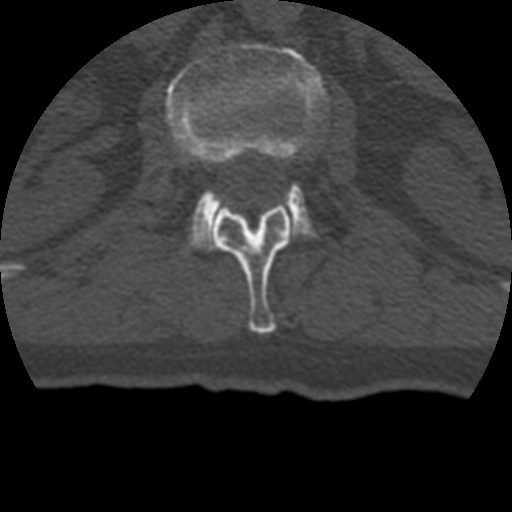
CT including the spine, one axial slice. Slice 133 of 399 in the series (ordered by position). Reconstruction kernel STANDARD. 120 kVp. Bone window (W 1800 / L 400 HU). 1.25 mm slice thickness. 512 × 512 image matrix, field of view 160 × 160 mm. Patient age 69 years. Case-level facts recorded for this patient, not image findings: primary cancer: prostate.
Annotated regions visible in this slice (semi-automatically segmented with operator editing):
- L1 vertebra: bounding box (x1, y1, x2, y2) in pixels: (212, 204, 293, 334)
- L2 vertebra: (166, 43, 326, 249)